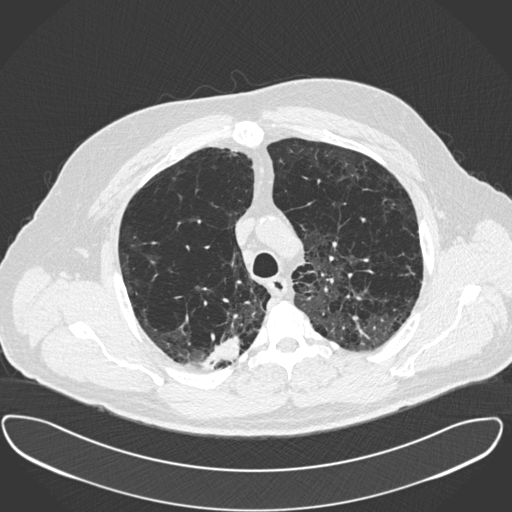
Low-dose screening chest CT, one axial slice. Slice 297 of 385 in the series (ordered by position). Reconstruction kernel B30f. 120 kVp. Lung window (W 1500 / L -600 HU). 512 × 512 image matrix.
Structures marked on this image (outlined manually by an expert reader):
- lesion 1 (tumor, upper lobe of right lung): box from (x=202, y=336) to (x=240, y=369) px